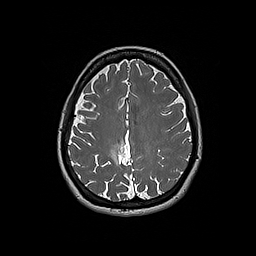
Brain MRI from a brain-tumour surgery series, one axial slice; 1 mm slice thickness; 256 × 256 image matrix. Case-level facts recorded for this patient, not image findings: histopathology: Oligodendroglioma; WHO grade: 2; IDH mutation: yes; tumour location: Right Parietal.
Structures marked on this image (manually delineated by an expert):
- tumour: bounding box <110,143,124,165> (left, top, right, bottom; pixels)